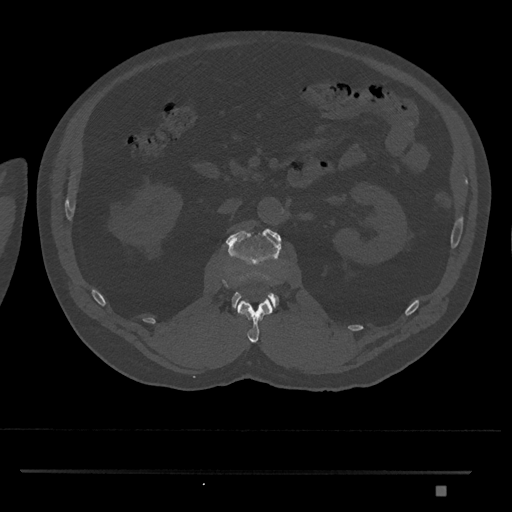
CT including the spine, one axial slice. Slice 790 of 1134 in the series (ordered by position). Reconstruction kernel Br40s/3. 120 kVp. Bone window (W 1800 / L 400 HU). 512 × 512 image matrix, field of view 429 × 429 mm. Patient: male, 65 years. Case-level facts recorded for this patient, not image findings: primary cancer: prostate.
Annotated regions visible in this slice (semi-automatic segmentation, software-assisted and operator-edited):
- L1 vertebra: bounding box [x1, y1, x2, y2] px = [237, 298, 273, 343]
- L2 vertebra: [226, 228, 282, 309]